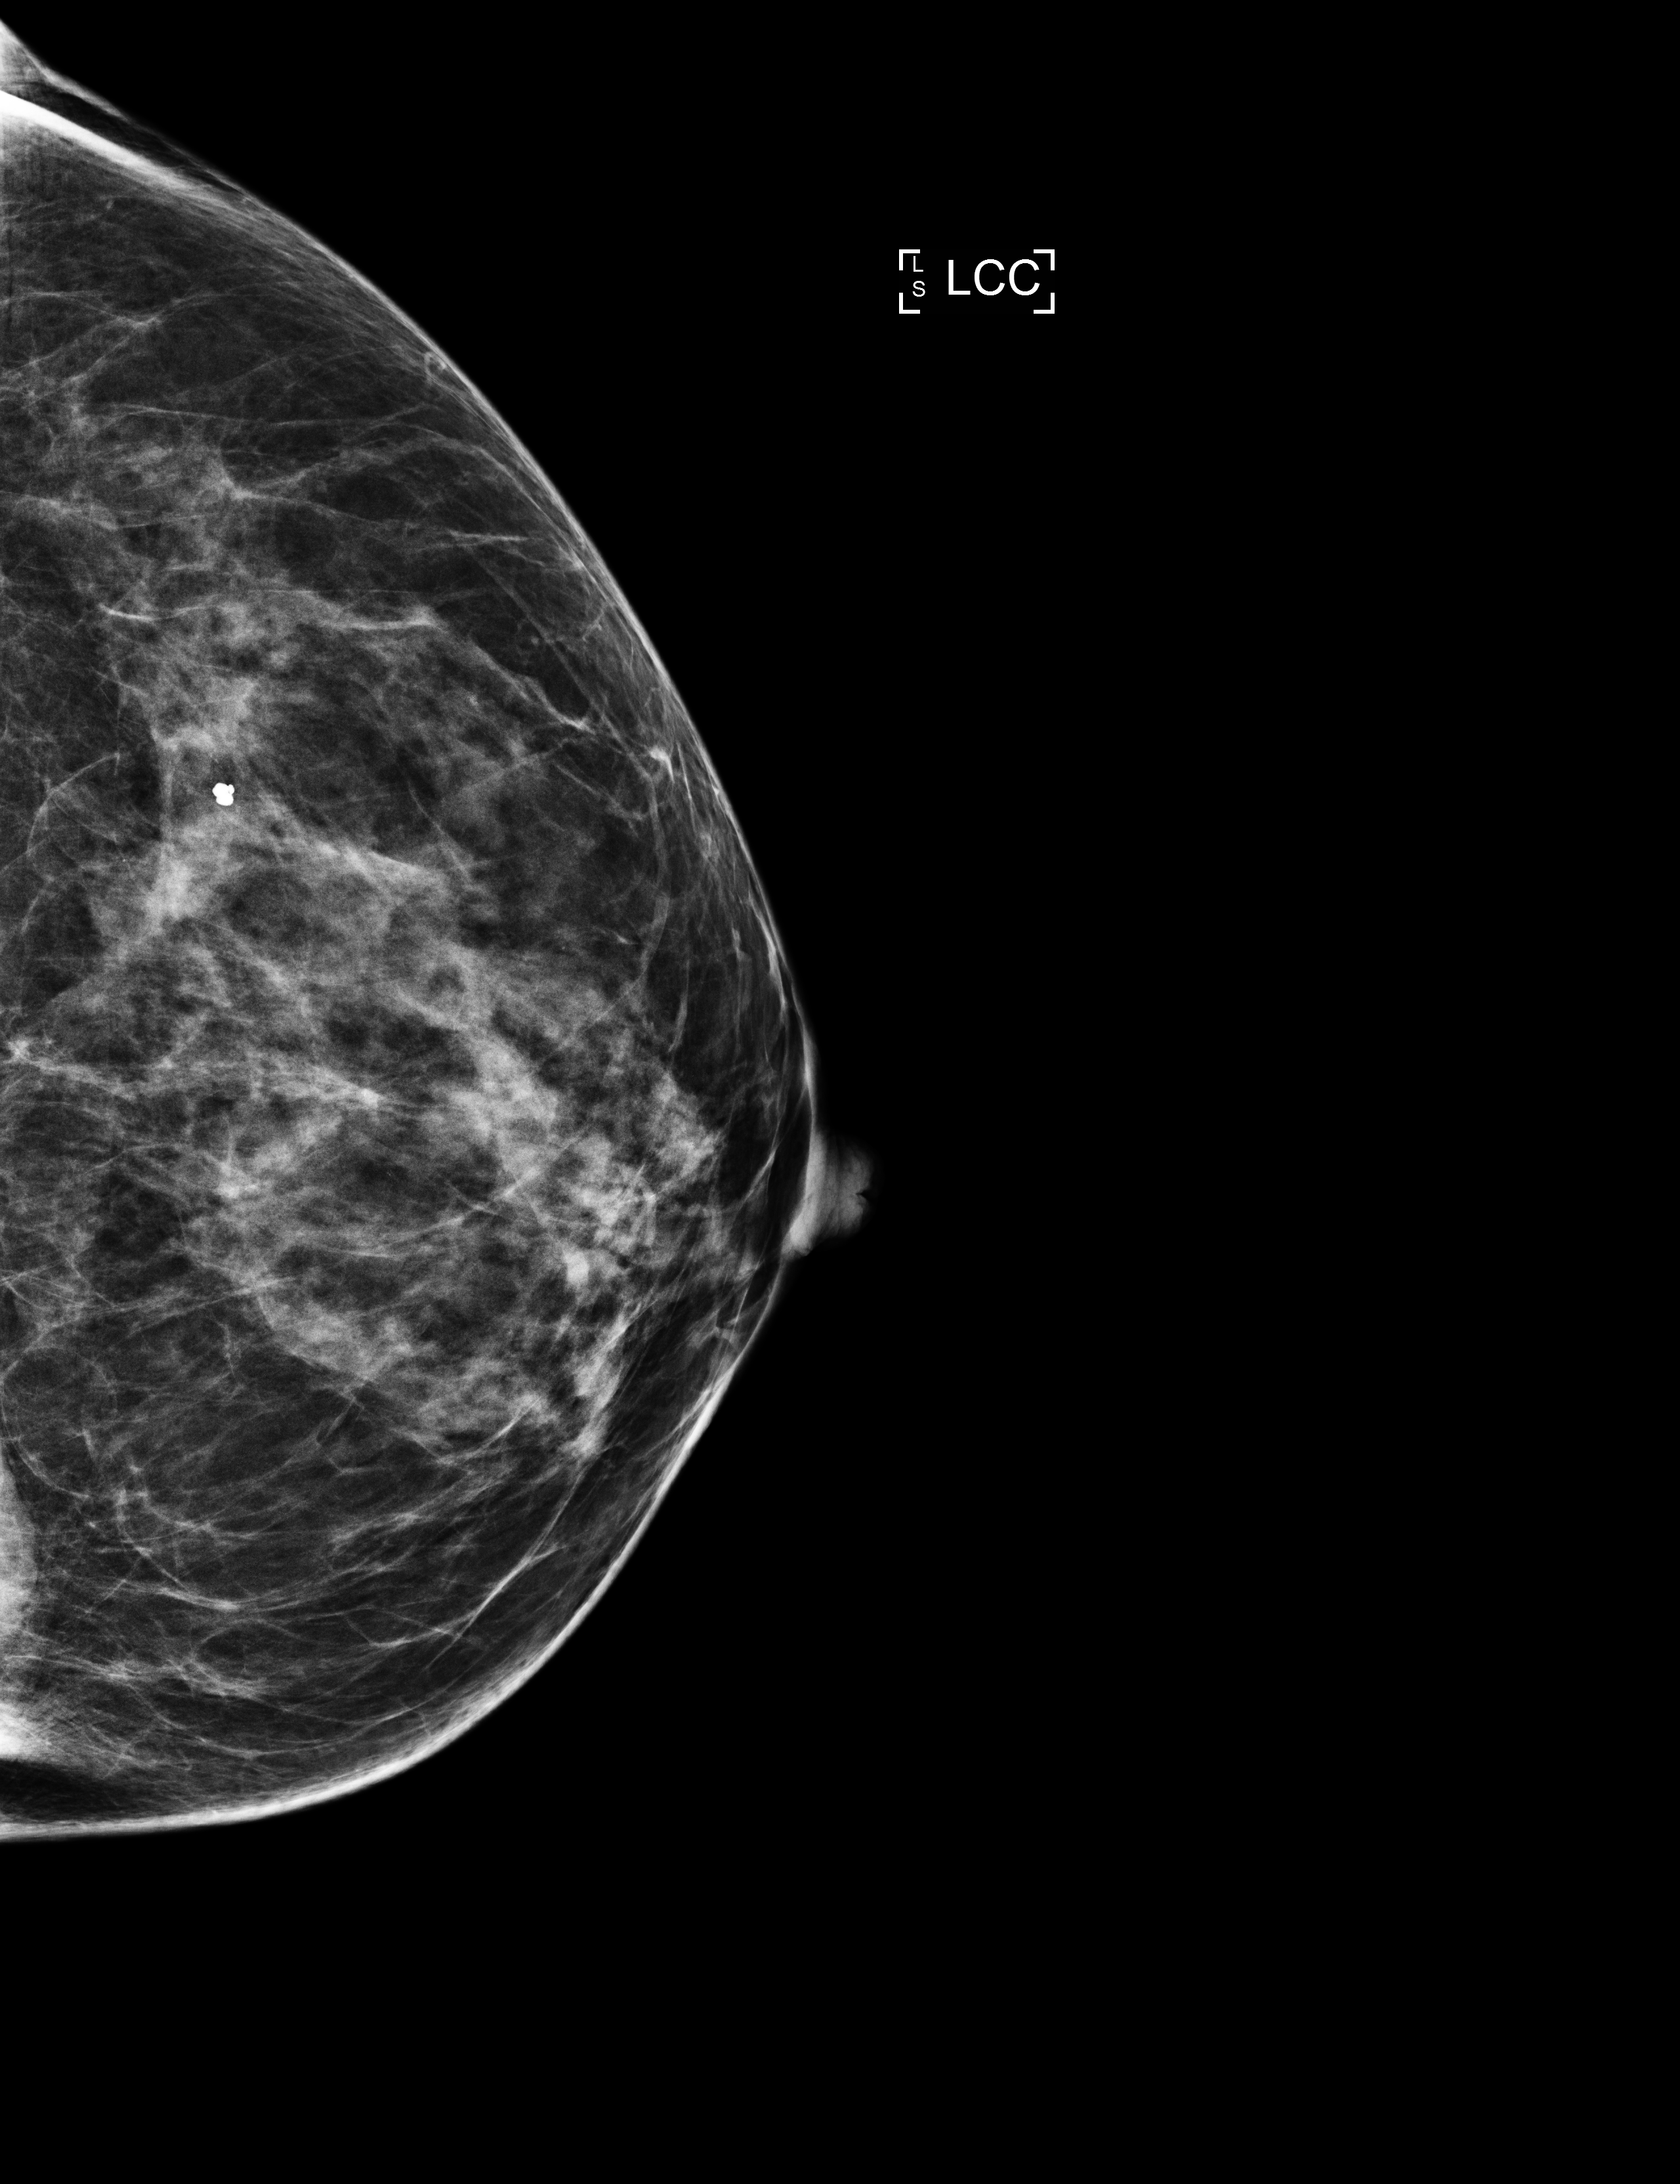
Screening examination; compressed breast thickness 58 mm. Patient: female, 61 years.
Image type: full-field digital mammogram. Breast: left. Projection: CC view.